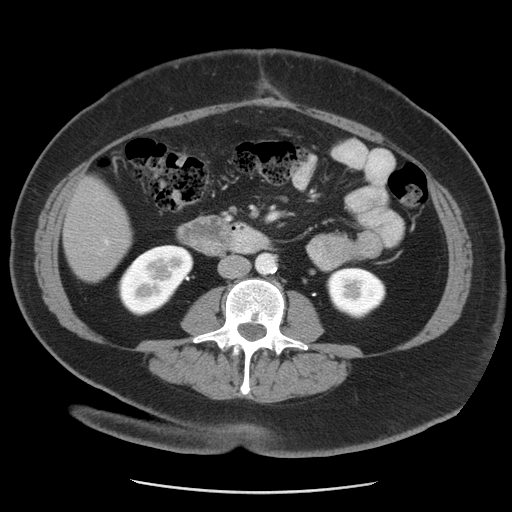
Contrast-enhanced abdominal CT, one axial slice; slice 9 of 55 in the series (ordered by position); reconstruction kernel STANDARD; intravenous contrast given; soft-tissue window (W 400 / L 40 HU); 5 mm slice thickness; 512 × 512 image matrix. Female patient, age 52 years. From the clinical record (not read from this slice): diagnosis: colorectal cancer liver metastases, imaged before liver resection; multiple liver metastases: yes.
Structures marked on this image (outlined manually by an expert reader):
- liver: bounding box <63,178,132,282> (left, top, right, bottom; pixels)
- planned liver remnant (the part of the liver to remain after resection): <63,197,128,282>
- portal vein (with intrahepatic branches): <95,194,117,255>